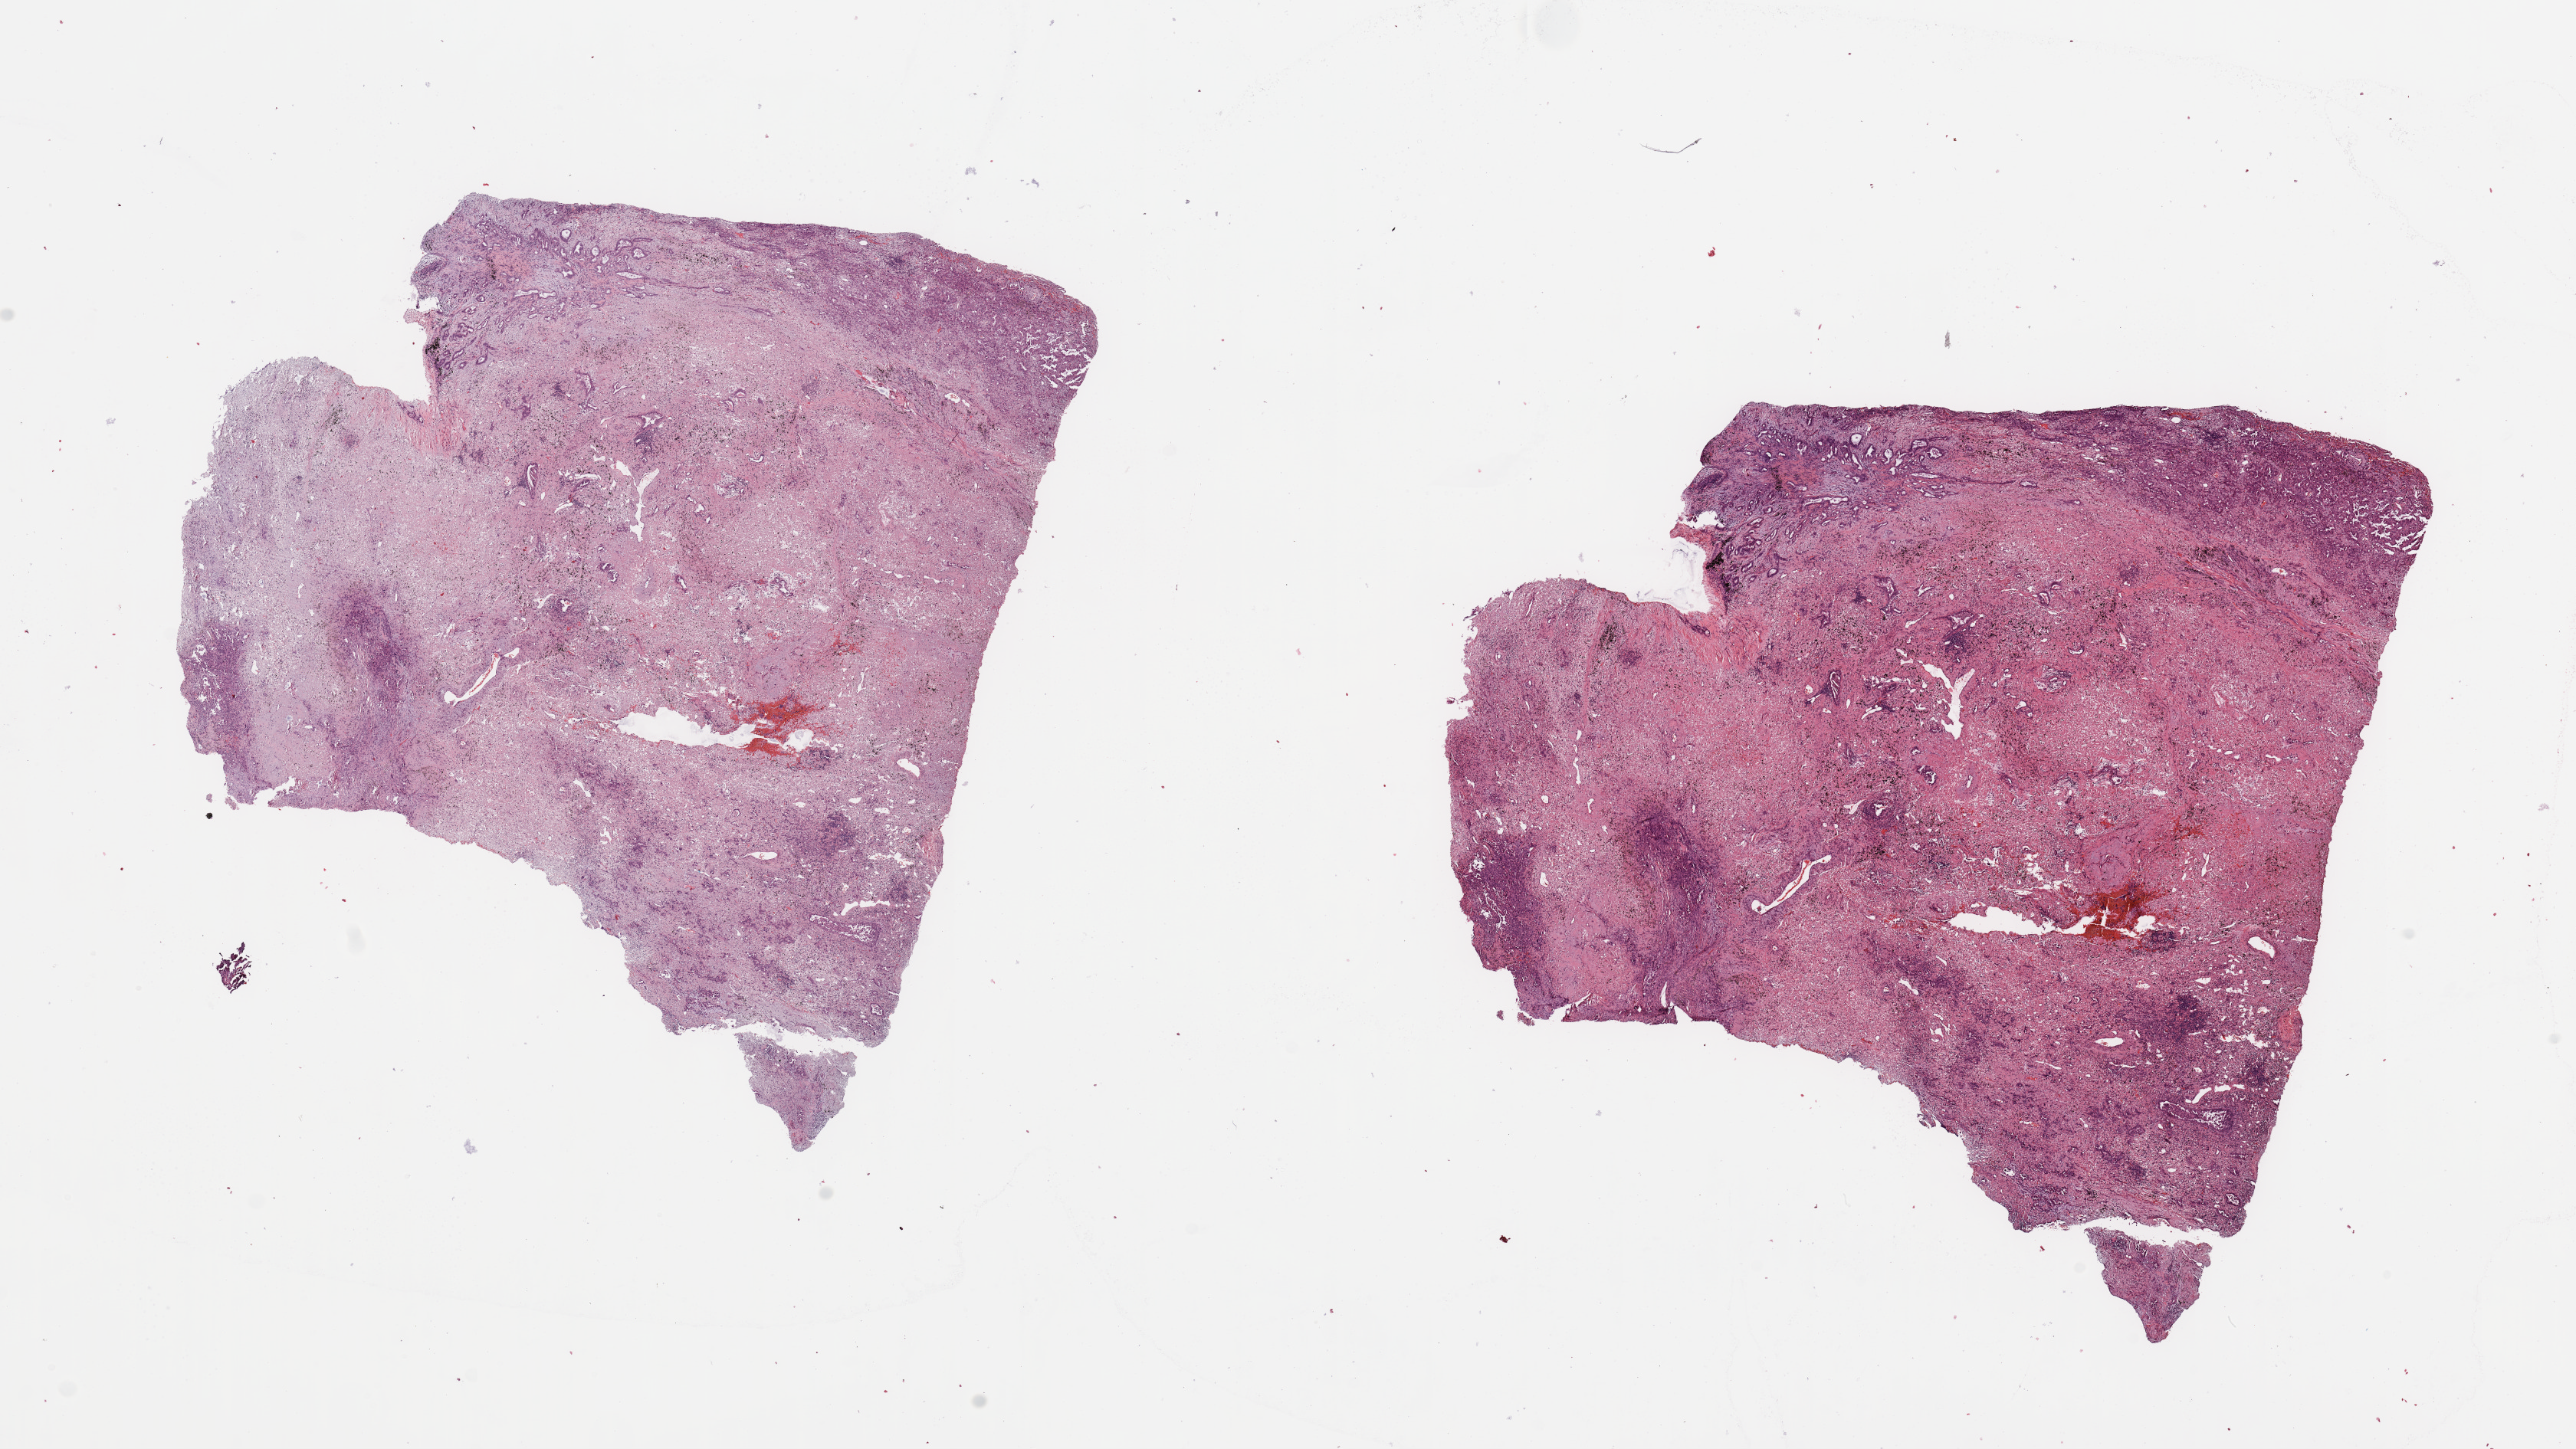
Whole-slide histology image, H&E-stained — low-resolution overview of the scanned area, about 26.6 x 15.0 mm. Lung, tumour tissue. Female, 67 y/o. Histologic grade: G2 (moderately differentiated).
• AJCC pathologic stage: II
• diagnosis: Adenocarcinoma, NOS